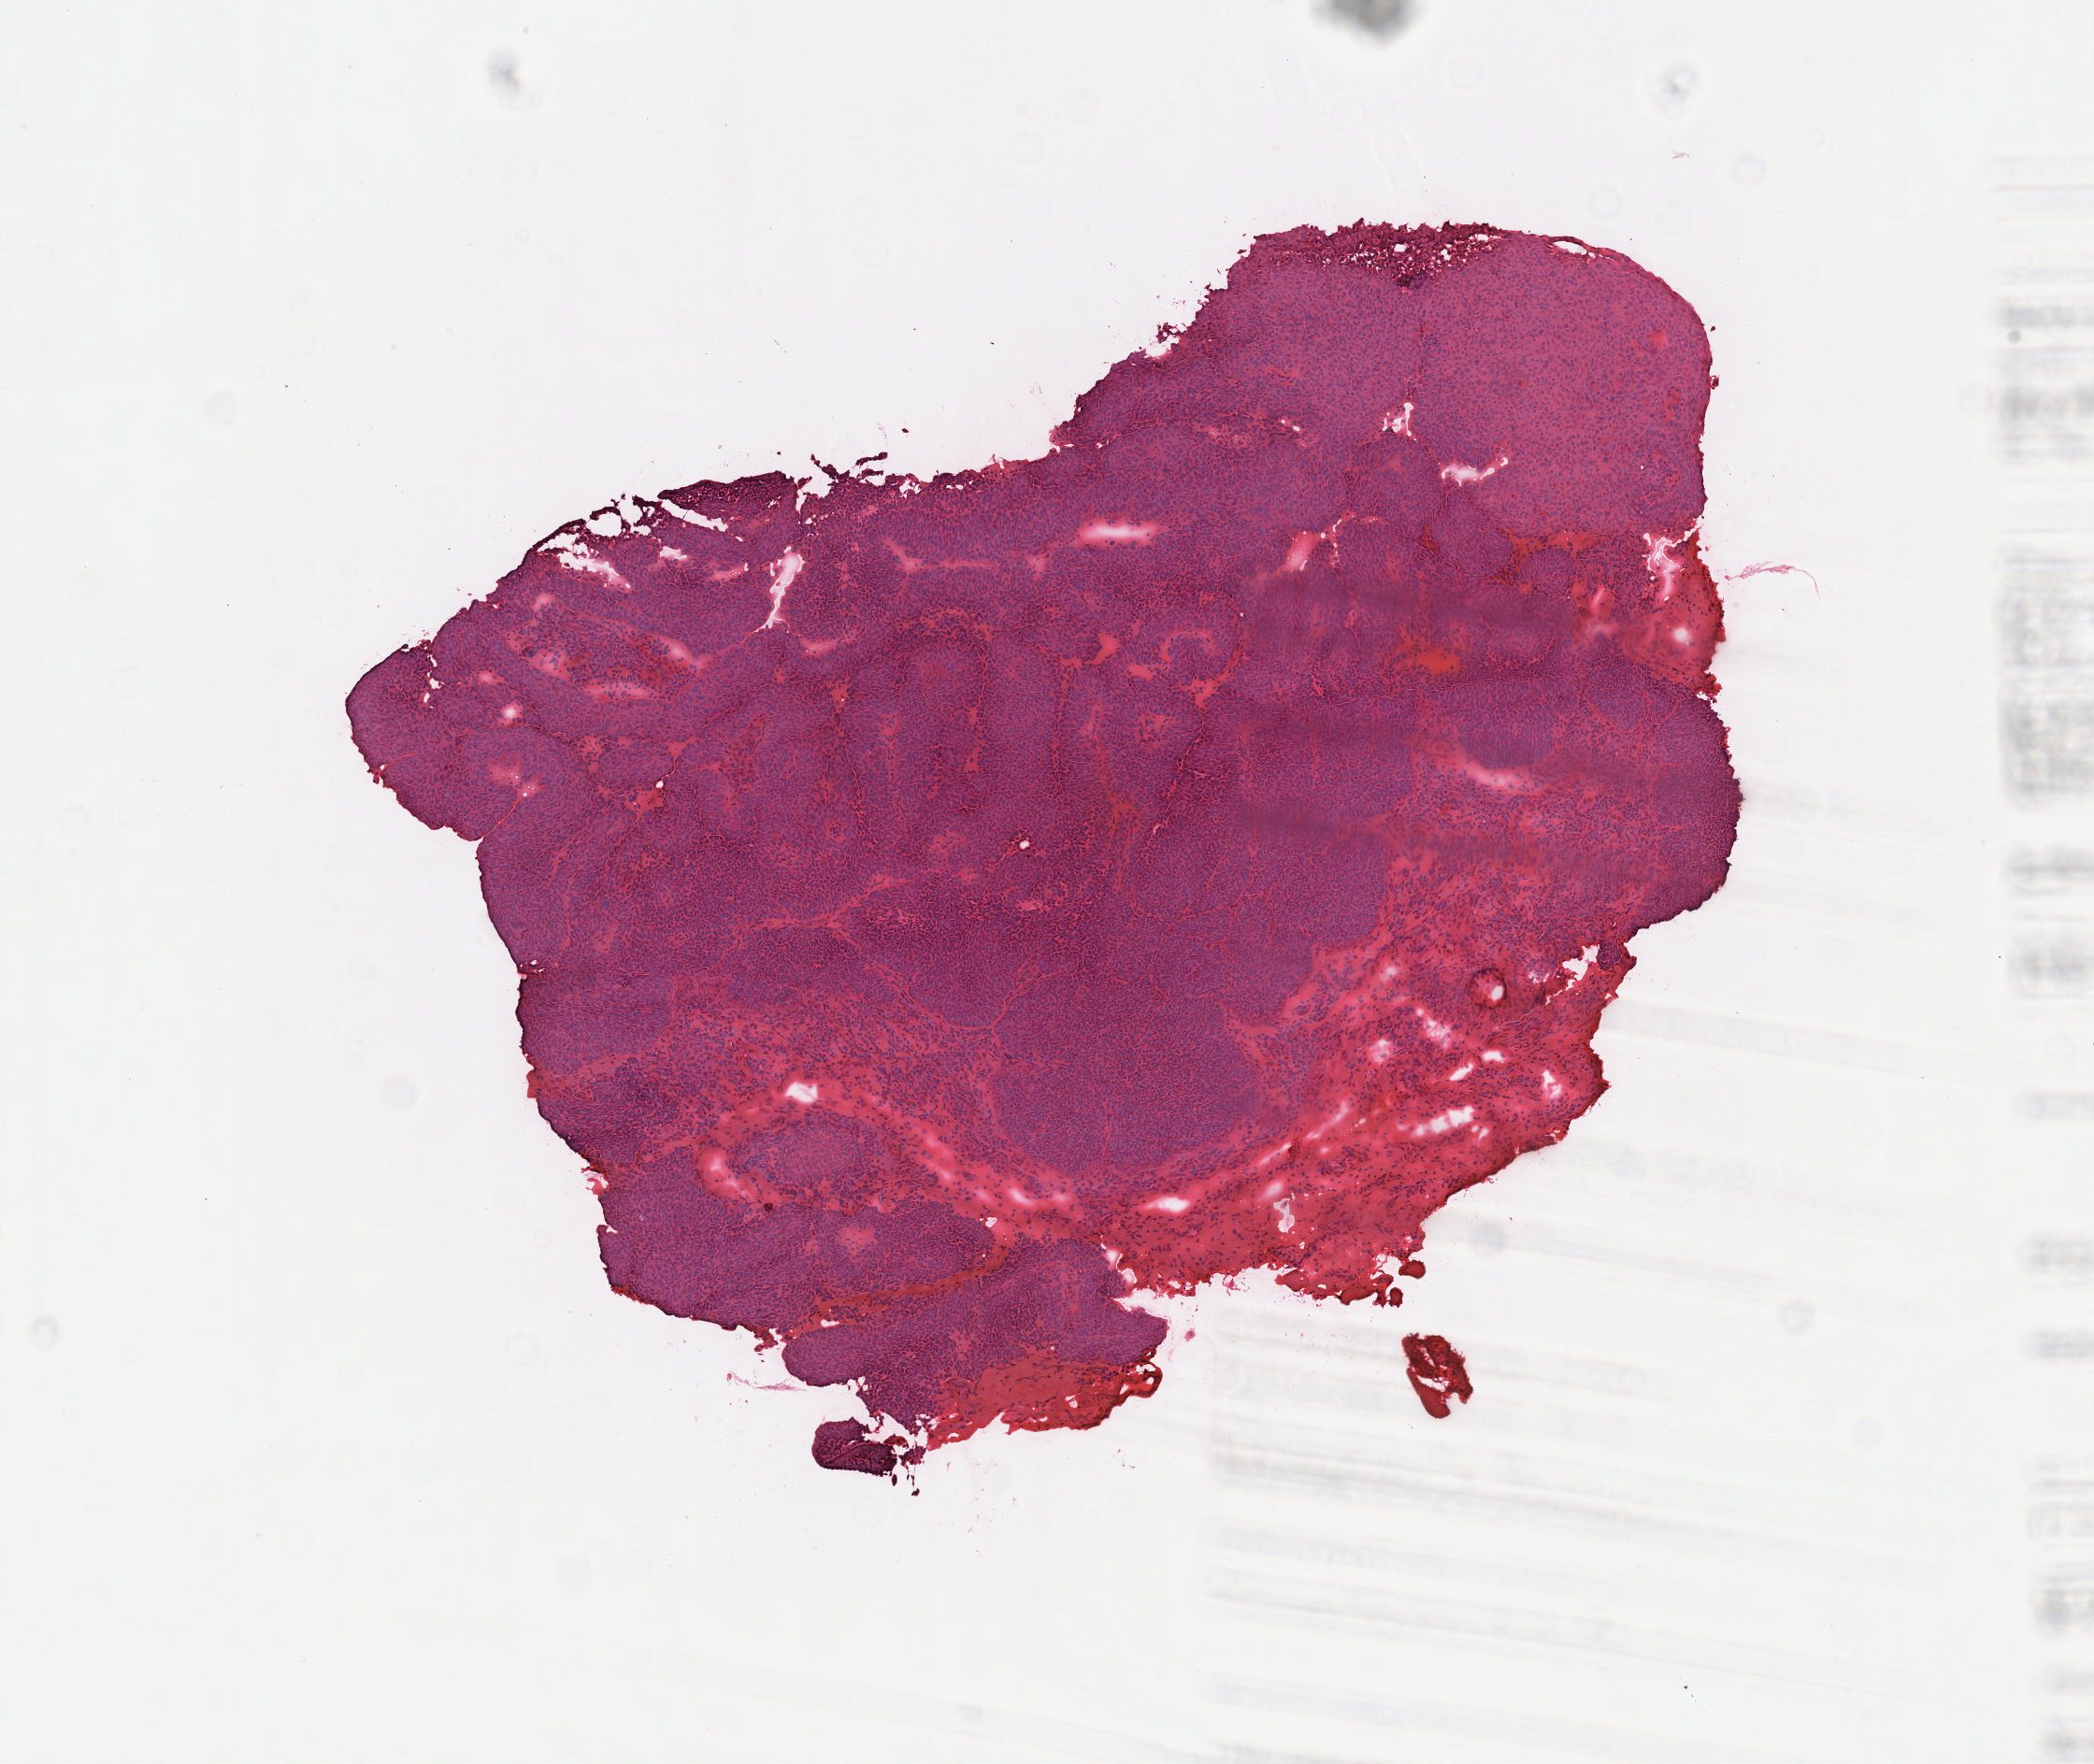
Whole-slide histology image, Hematoxylin and eosin (H&E) stained — shown as a low-resolution overview of the whole scanned area (about 4.5 x 3.8 mm, acquisition: 40x scan). Frozen section from the top of the tissue portion. Primary tumour sample from the head and neck. Patient: male, age at initial diagnosis 69 years. Histologic grade: G3 (poorly differentiated). Slide review estimates, as recorded: tumour cells 80%, tumour nuclei 80%, normal cells 0%, stromal cells 20%, necrosis 0%. Inflammatory infiltration, as recorded: lymphocyte infiltration 3%, monocyte infiltration 1%, neutrophil infiltration 4%.
Laterality: right. AJCC pathologic stage: I (7th edition). Pathologic diagnosis: Basaloid squamous cell carcinoma (larynx, NOS).